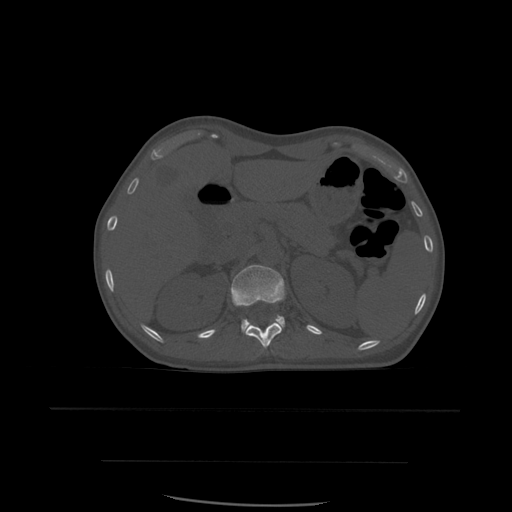
CT including the spine, one axial slice. Position 263 of 574 along the scan axis. Bone window (W 1800 / L 400 HU). 512 × 512 image matrix, field of view 392 × 392 mm. Patient age 48 years. Case-level facts recorded for this patient, not image findings: primary cancer: lung; vertebrae with lytic lesions (as recorded): T11.
Structures marked on this image (semi-automatically segmented with operator editing):
- L1 vertebra: bounding box <231,265,285,334> (left, top, right, bottom; pixels)
- T12 vertebra: <246,323,282,350>